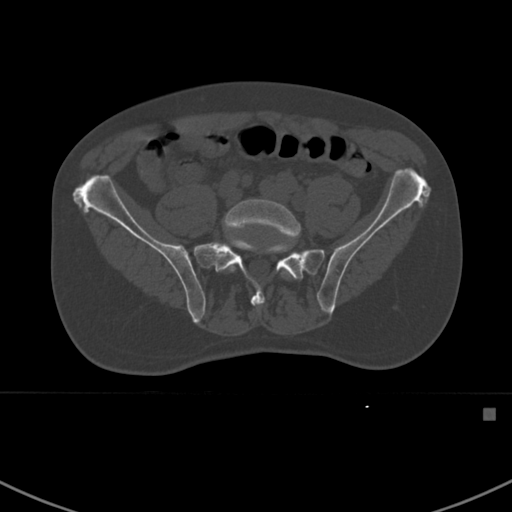
CT including the spine, one axial slice. Slice 209 of 412 in the series (ordered by position). Reconstruction kernel Br40s. 120 kVp. Bone window (W 1800 / L 400 HU). 1.5 mm slice thickness. 512 × 512 image matrix, field of view 358 × 358 mm. Patient: male, 59 years. From the clinical record (not read from this slice): primary cancer: prostate.
Outlined on this slice (semi-automatic segmentation, software-assisted and operator-edited):
- L5 vertebra: bounding box (x1, y1, x2, y2) in pixels: (223, 199, 301, 279)